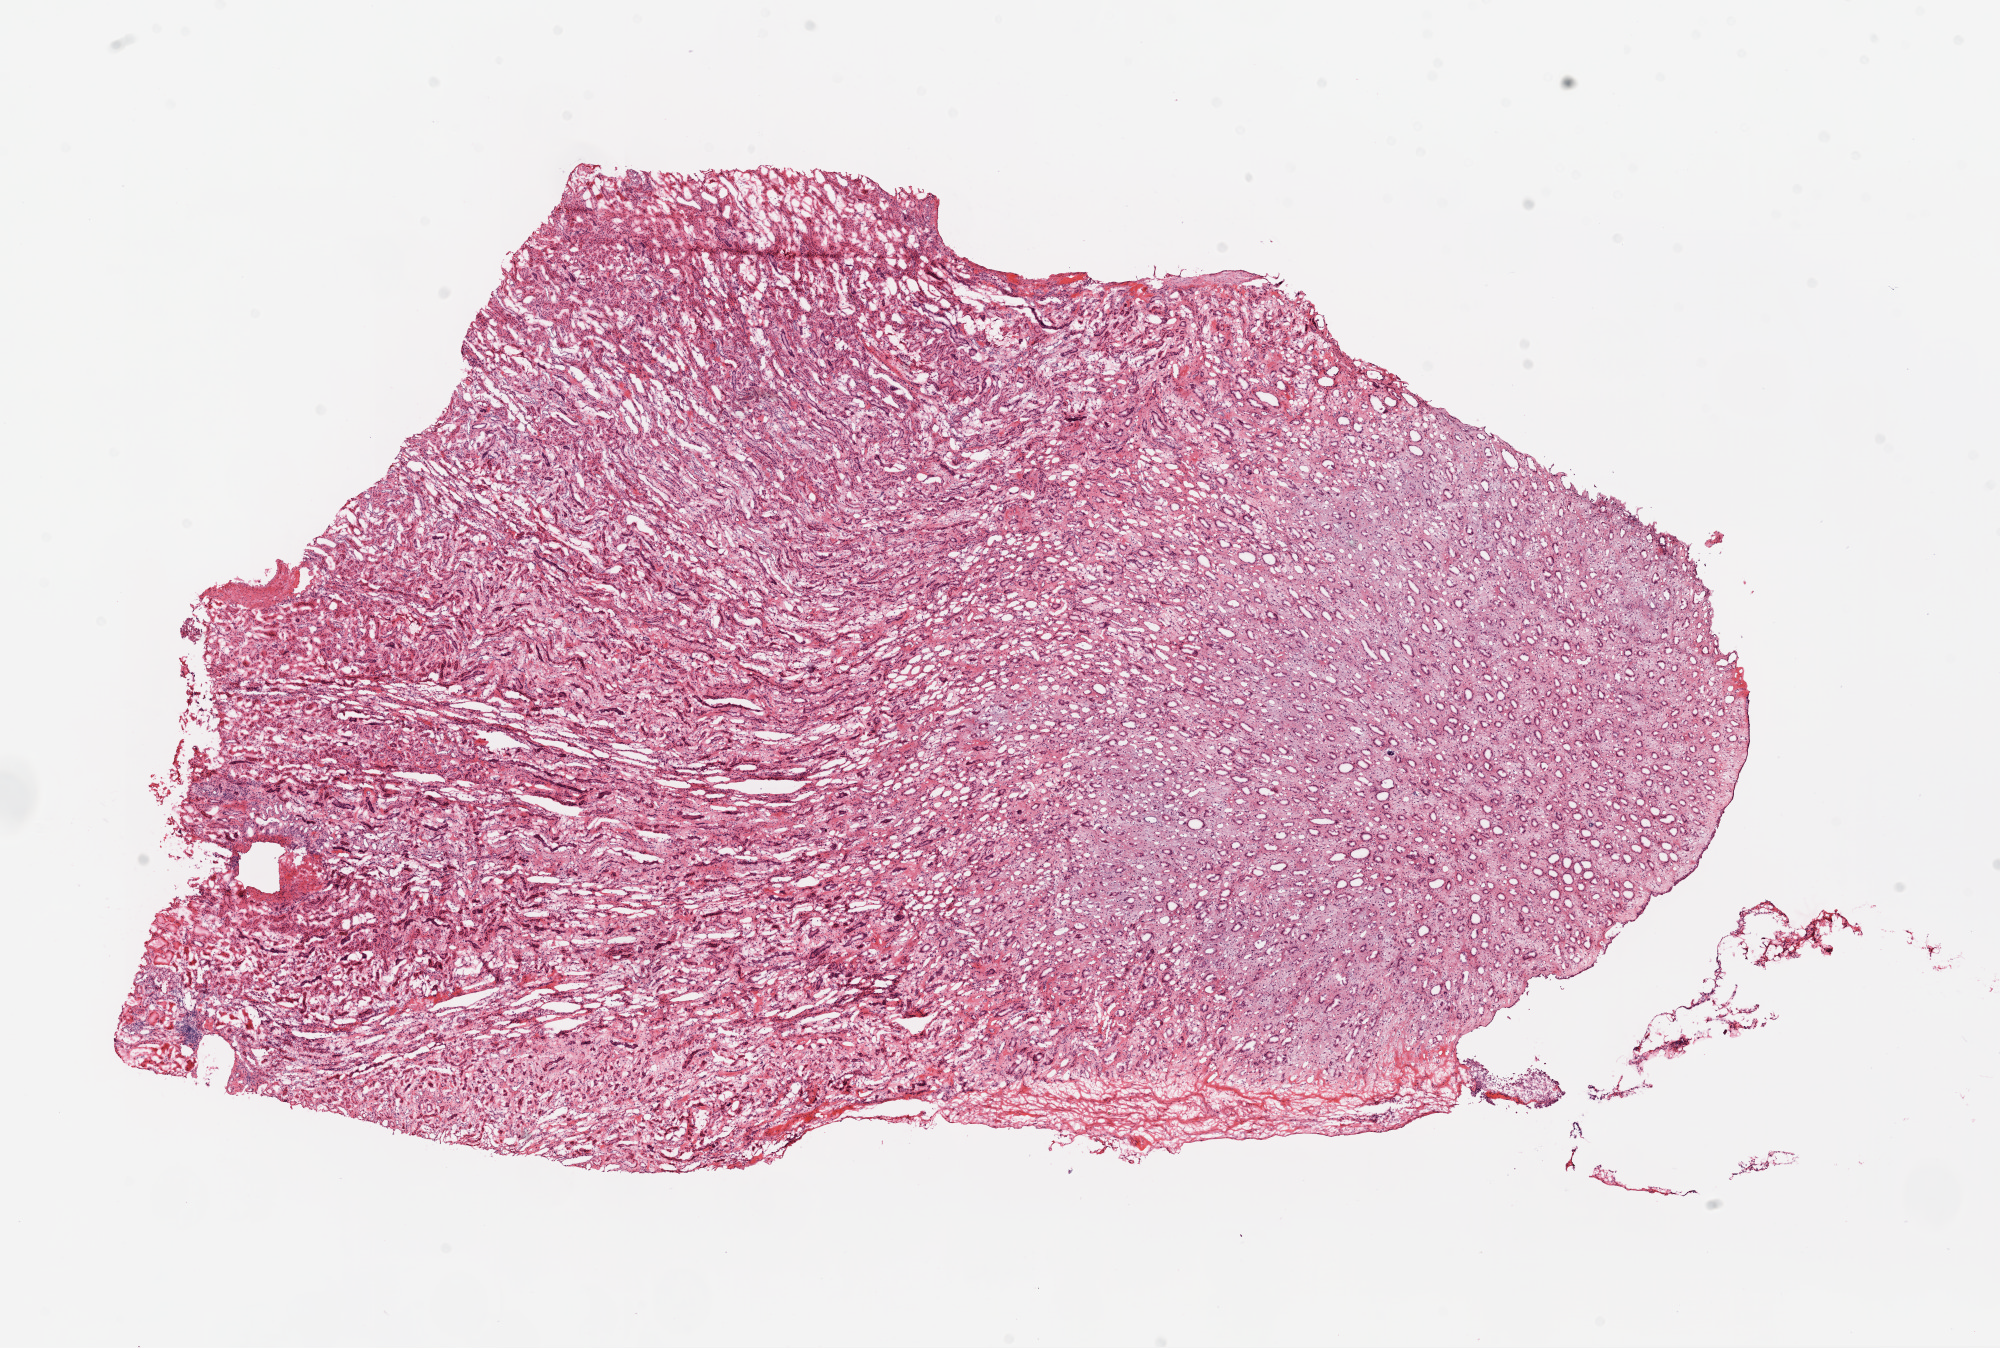
Whole-slide histology image, Hematoxylin and eosin (H&E) stained — low-resolution overview of the scanned area, about 16.0 x 10.8 mm (slide scanned at 20x); frozen section from the top of the tissue portion; kidney, solid tissue normal (non-tumour tissue) sample. Male patient; age at initial diagnosis 46 years.
* this section: solid tissue normal sample (biorepository sample class)
* patient diagnosis: Clear cell adenocarcinoma, NOS